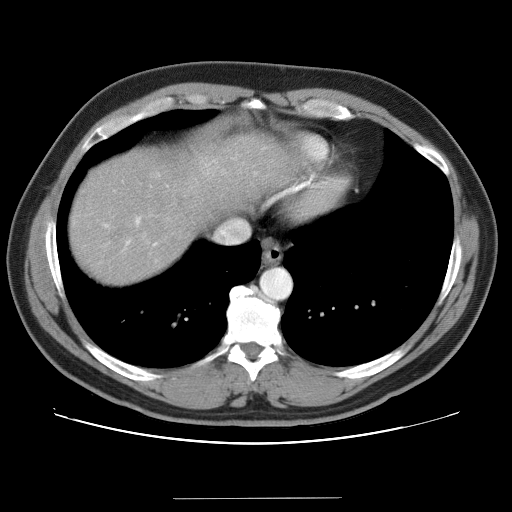
Contrast-enhanced abdominal CT (liver protocol), one axial slice. Position 34 of 40 along the scan axis. 120 kVp. Soft-tissue window (W 400 / L 40 HU). 512 × 512 image matrix. From the clinical record (not read from this slice): diagnosis: hepatocellular carcinoma (patient treated with transarterial chemoembolisation; whether this scan precedes or follows treatment is not stated here); TNM stage (as recorded): Stage-IVA; Child-Pugh class: B.
Outlined on this slice (semi-automatically segmented with operator editing):
- liver parenchyma outside the tumour (the mass and vessels are separate outlines, so this box may not span the whole liver): bounding box (x1, y1, x2, y2) in pixels: (70, 134, 298, 282)
- liver vessels: (126, 218, 155, 245)